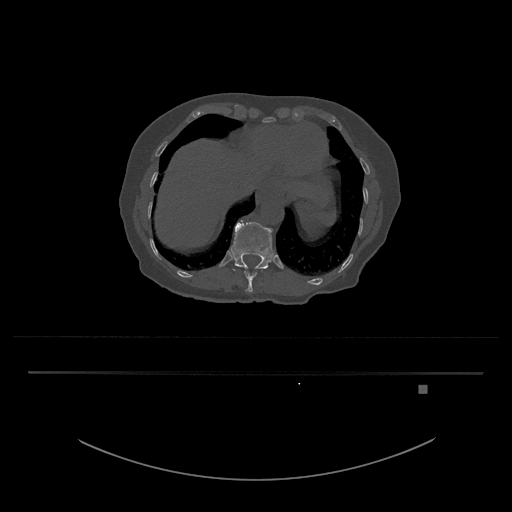
CT including the spine, one axial slice; 120 kVp; bone window (W 1800 / L 400 HU); 0.5 mm slice thickness; 512 × 512 image matrix. Female patient, age 57 years. From the clinical record (not read from this slice): primary cancer: cervical.
Outlined on this slice (semi-automatic segmentation, software-assisted and operator-edited):
- T11 vertebra: bounding box [x1, y1, x2, y2] px = [244, 267, 264, 292]
- T12 vertebra: [231, 222, 274, 272]